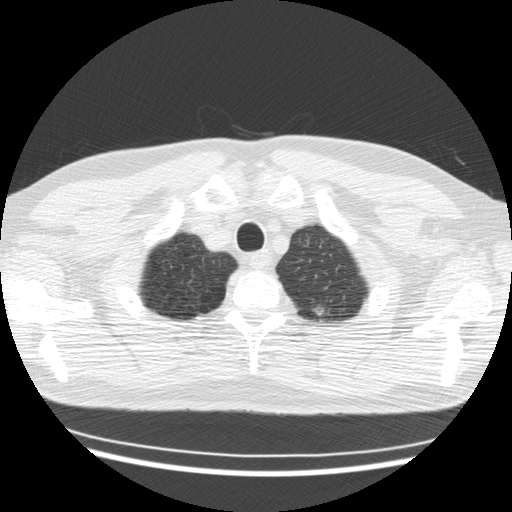
Low-dose screening chest CT, one axial slice. Slice 156 of 176 in the series (ordered by position). Reconstruction kernel STANDARD. 120 kVp. Lung window (W 1500 / L -600 HU). 2.5 mm slice thickness. 512 × 512 image matrix, field of view 360 × 360 mm.
Annotated regions visible in this slice (expert manual segmentation):
- lesion 1 (tumor, upper lobe of left lung): bounding box <315,304,325,317> (left, top, right, bottom; pixels)